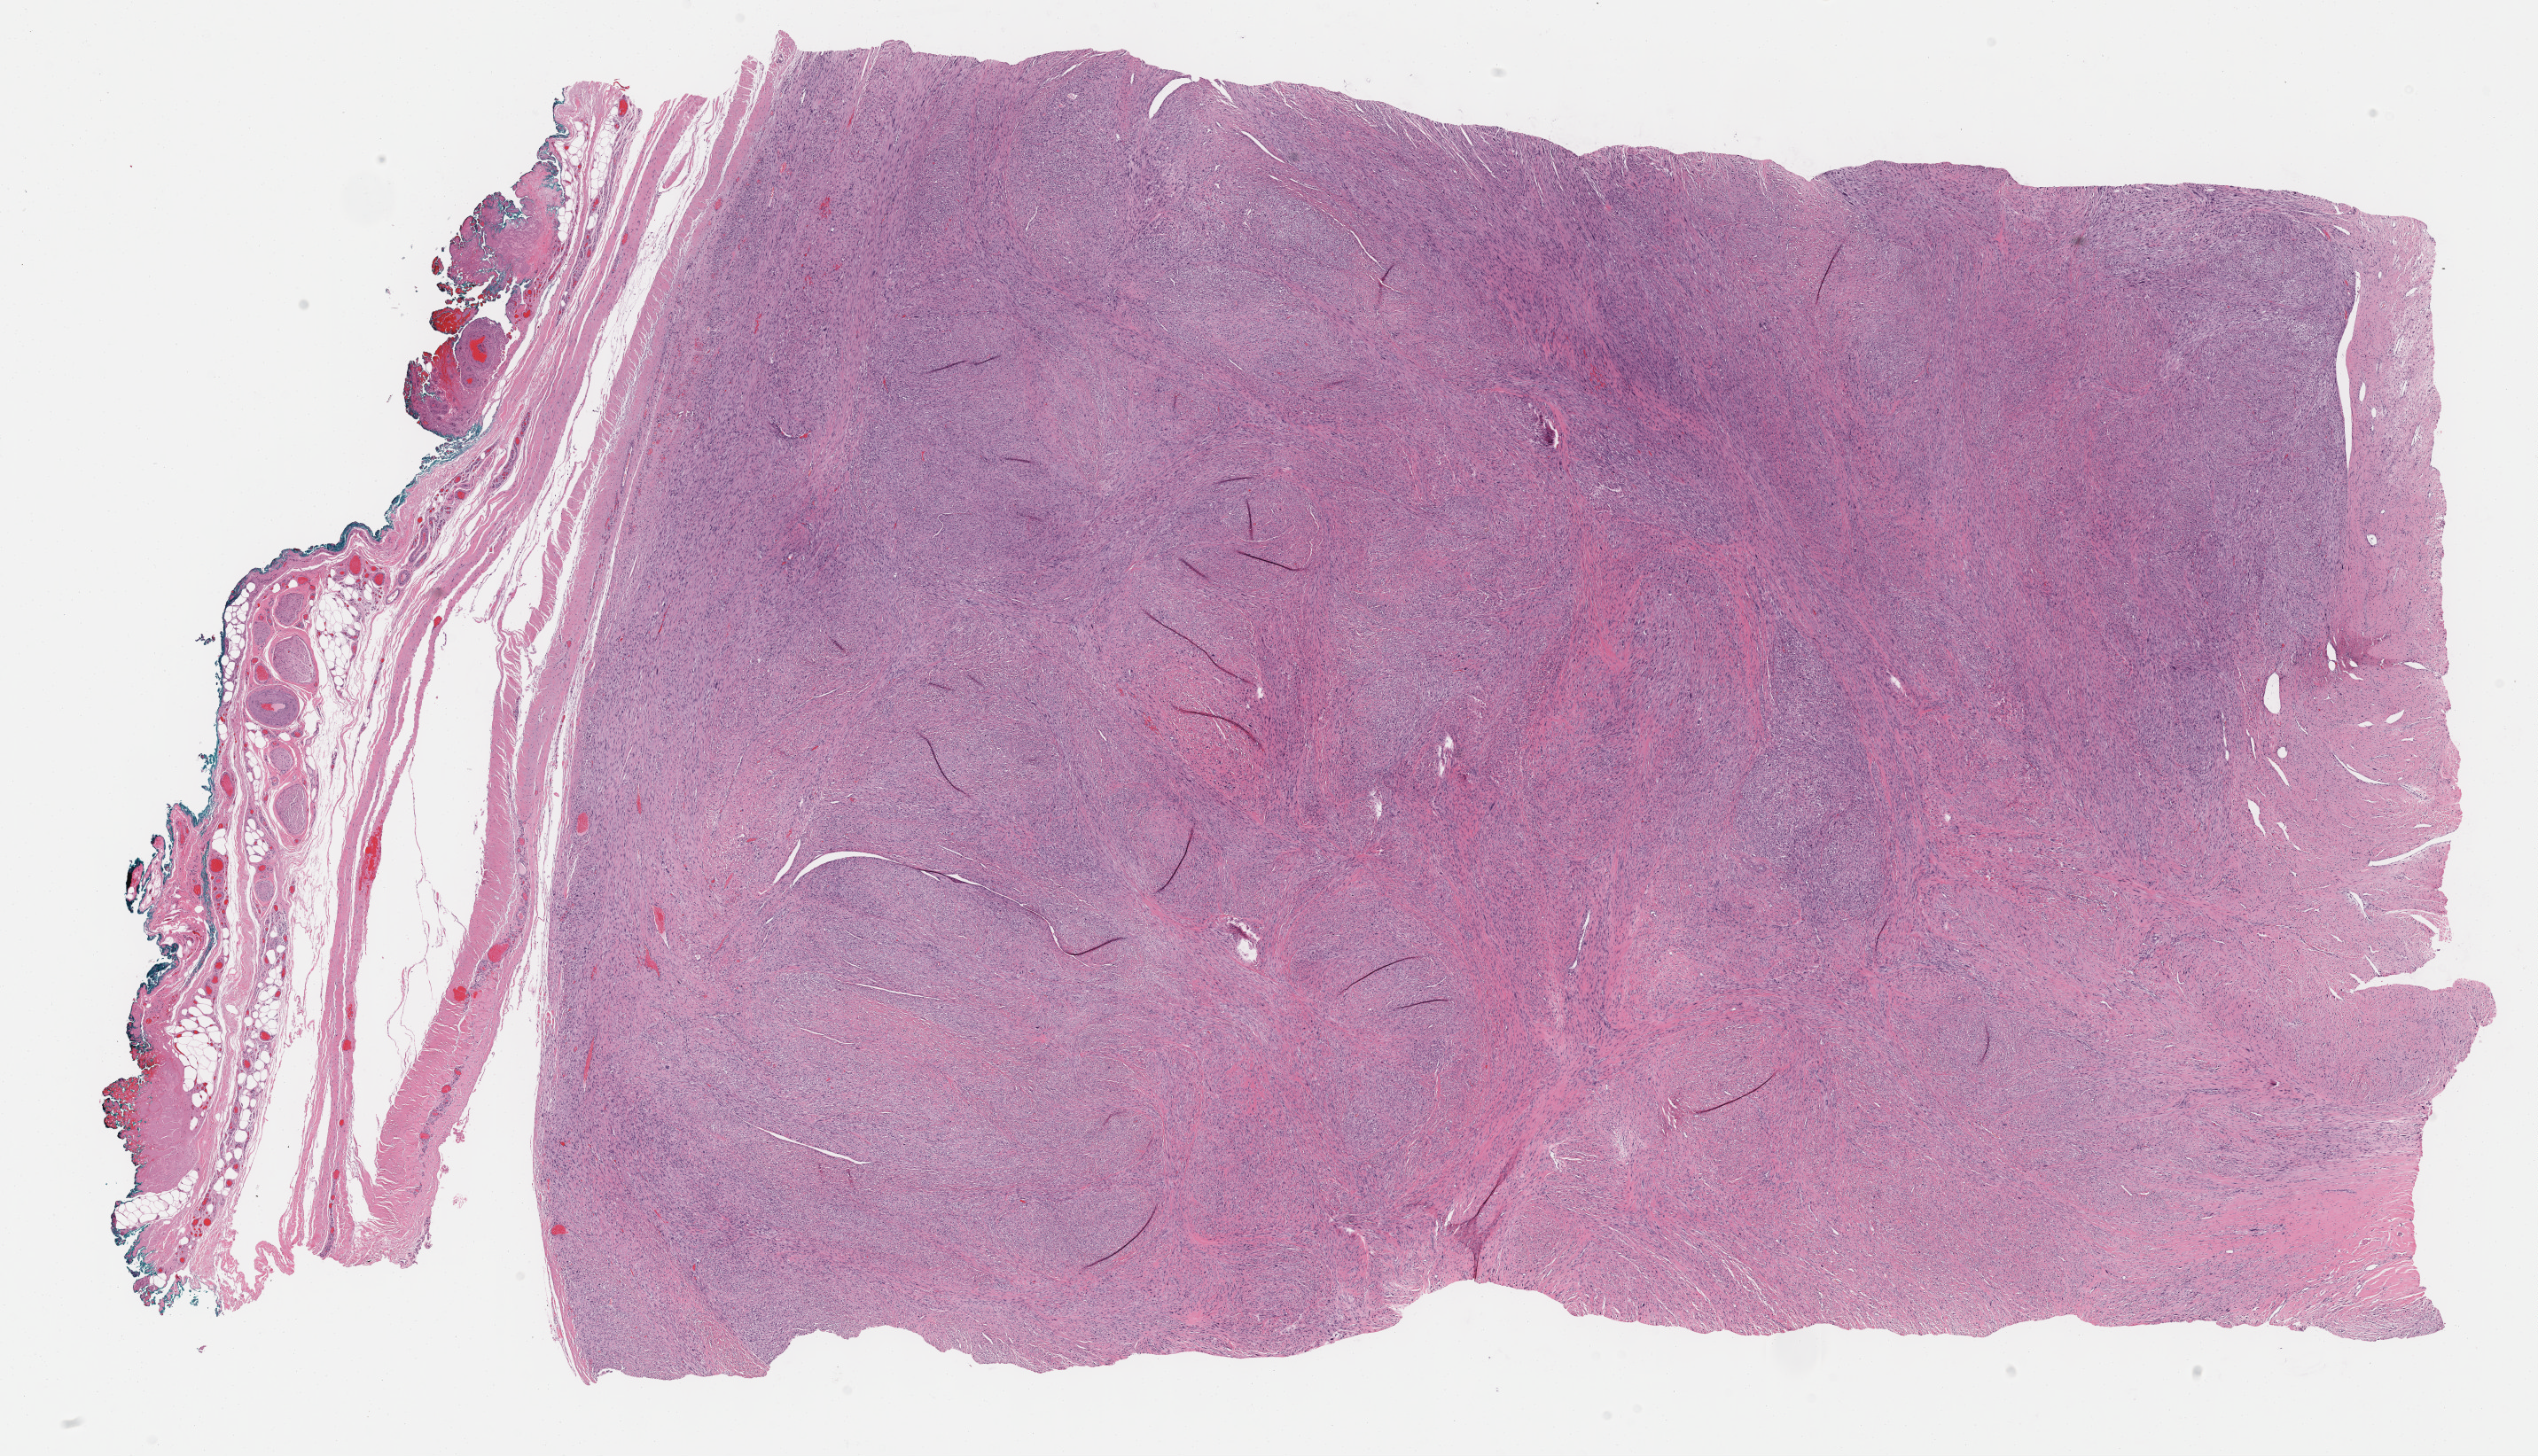
Hematoxylin and eosin (H&E) stained whole-slide image, low-resolution overview of the scanned area, about 23.2 x 13.3 mm (from a 40x scan). Formalin-fixed paraffin-embedded (FFPE) diagnostic section. Sample: primary tumour, connective, subcutaneous and other soft tissues. Male patient; age at initial diagnosis 65 years.
Pathologic diagnosis: Leiomyosarcoma, NOS (connective, subcutaneous and other soft tissues of lower limb and hip).